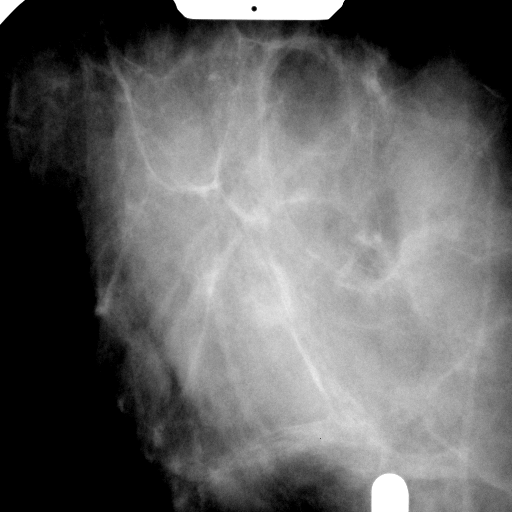
Spot-compression mammographic view.
Pathology recorded for this patient (not read from this image): pathology diagnosis: benign fibroadenoma (right breast); pathology report notes: RIGHT BREAST CALCIFICATION WITH NEEDLE LOCATION: FIBROADENOMA (1.9CM). REMAINING BREAST TISSUE WITH ADENOSIS, FOCAL FIBROADENOMATOUS CHANGES, APOCRINE METAPLASIA, FIBROCYSTIC CHANGES, SMALL INTRADUCTAL PAPILLOMAS, AND USUAL TYPE DUCTAL HYPERPLASIA. MICROCALCIFICATIONS ASSOCIATED WITH BENIGN BREAST TISSUE ARE IDENTIFIED. NO IN-SITU OR INVASIVE CARCINOMA.